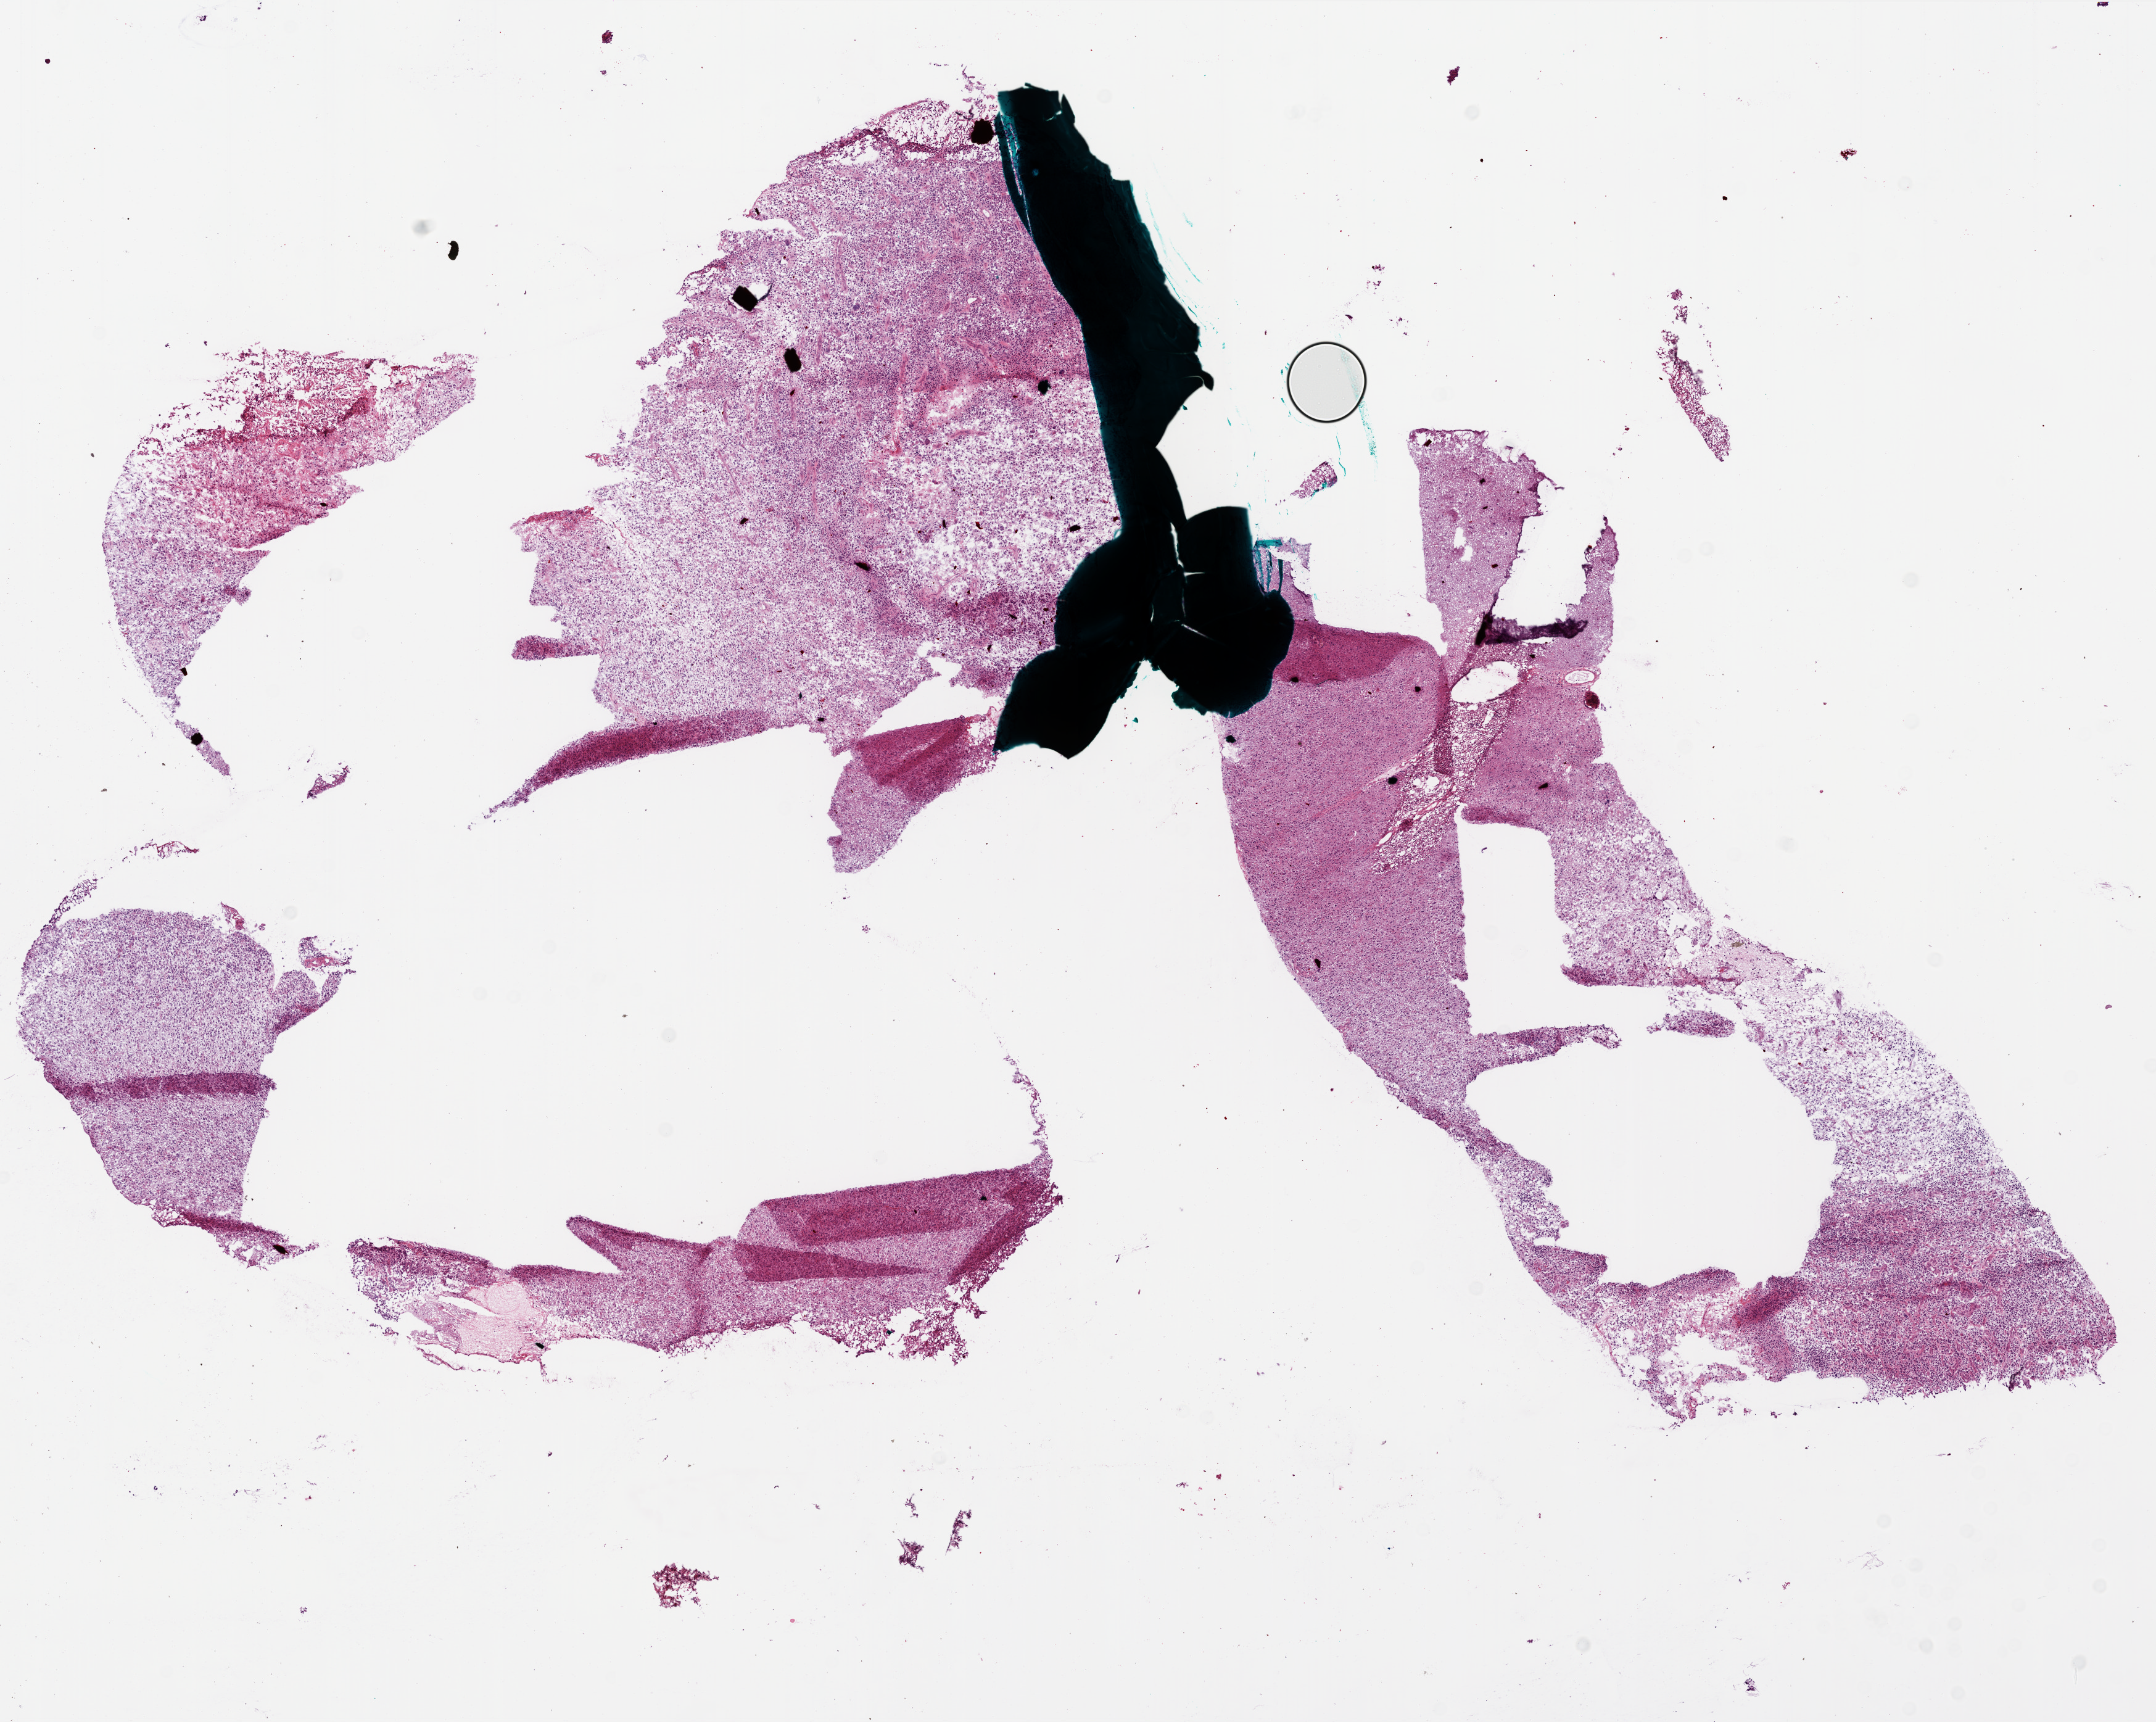
Whole-slide histology image, H&E-stained — low-resolution overview of the scanned area, about 14.0 x 11.2 mm; frozen section from the bottom of the tissue portion; primary tumour sample from the brain. Patient: female, age at initial diagnosis 69 years.
Pathologic diagnosis: Glioblastoma.